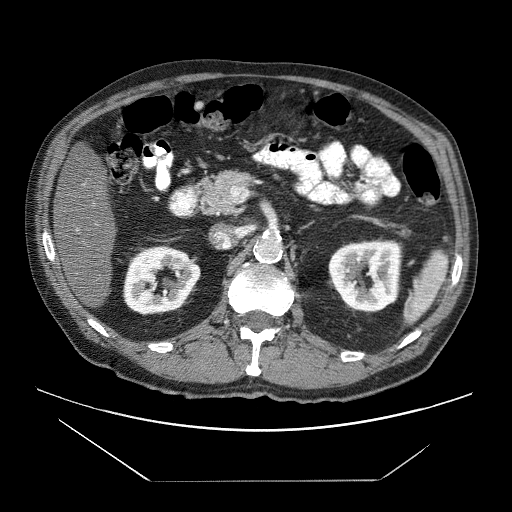
Contrast-enhanced abdominal CT (liver protocol), one axial slice; position 21 of 83 along the scan axis; reconstruction kernel STANDARD; 120 kVp; soft-tissue window (W 400 / L 40 HU); 512 × 512 image matrix, field of view 420 × 420 mm. From the clinical record (not read from this slice): diagnosis: hepatocellular carcinoma (patient treated with transarterial chemoembolisation; whether this scan precedes or follows treatment is not stated here); TNM stage (as recorded): Stage-IVB; Child-Pugh class: B; tumour differentiation: poorly differentiated.
Structures marked on this image (semi-automatic segmentation, software-assisted and operator-edited):
- liver parenchyma outside the tumour (the mass and vessels are separate outlines, so this box may not span the whole liver): box from (x=52, y=153) to (x=116, y=306) px